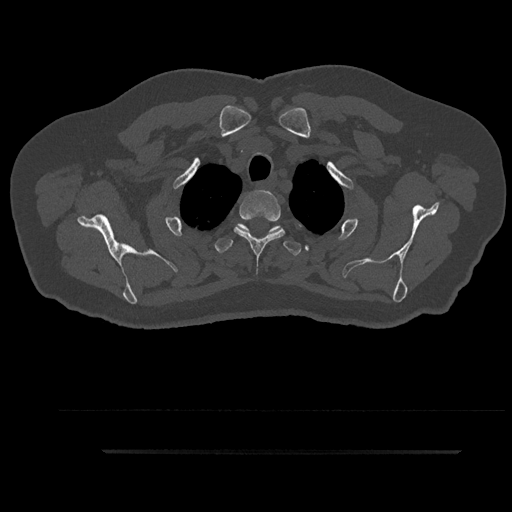
CT including the spine, one axial slice. Slice 748 of 797 in the series (ordered by position). 120 kVp. Bone window (W 1800 / L 400 HU). 0.5 mm slice thickness. 512 × 512 image matrix. Male patient, age 63 years. Case-level facts recorded for this patient, not image findings: primary cancer: renal; vertebrae with lytic lesions (as recorded): T8.
Outlined on this slice (semi-automatically segmented with operator editing):
- T2 vertebra: bounding box [x1, y1, x2, y2] px = [234, 190, 285, 260]
- T3 vertebra: [215, 224, 302, 256]